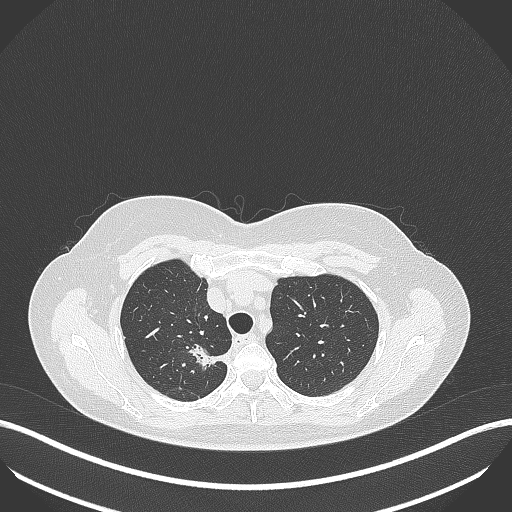
Chest CT, one axial slice. Position 309 of 386 along the scan axis. Lung window (W 1500 / L -600 HU). 512 × 512 image matrix, field of view 400 × 400 mm. Patient: female, 65 years. From the clinical record (not read from this slice): clinical TNM (as recorded): T1b N0 M0.
Outlined on this slice (bounding box drawn by a radiologist):
- lung tumour (recorded histology: adenocarcinoma): bounding box (x1, y1, x2, y2) in pixels: (187, 341, 232, 375)